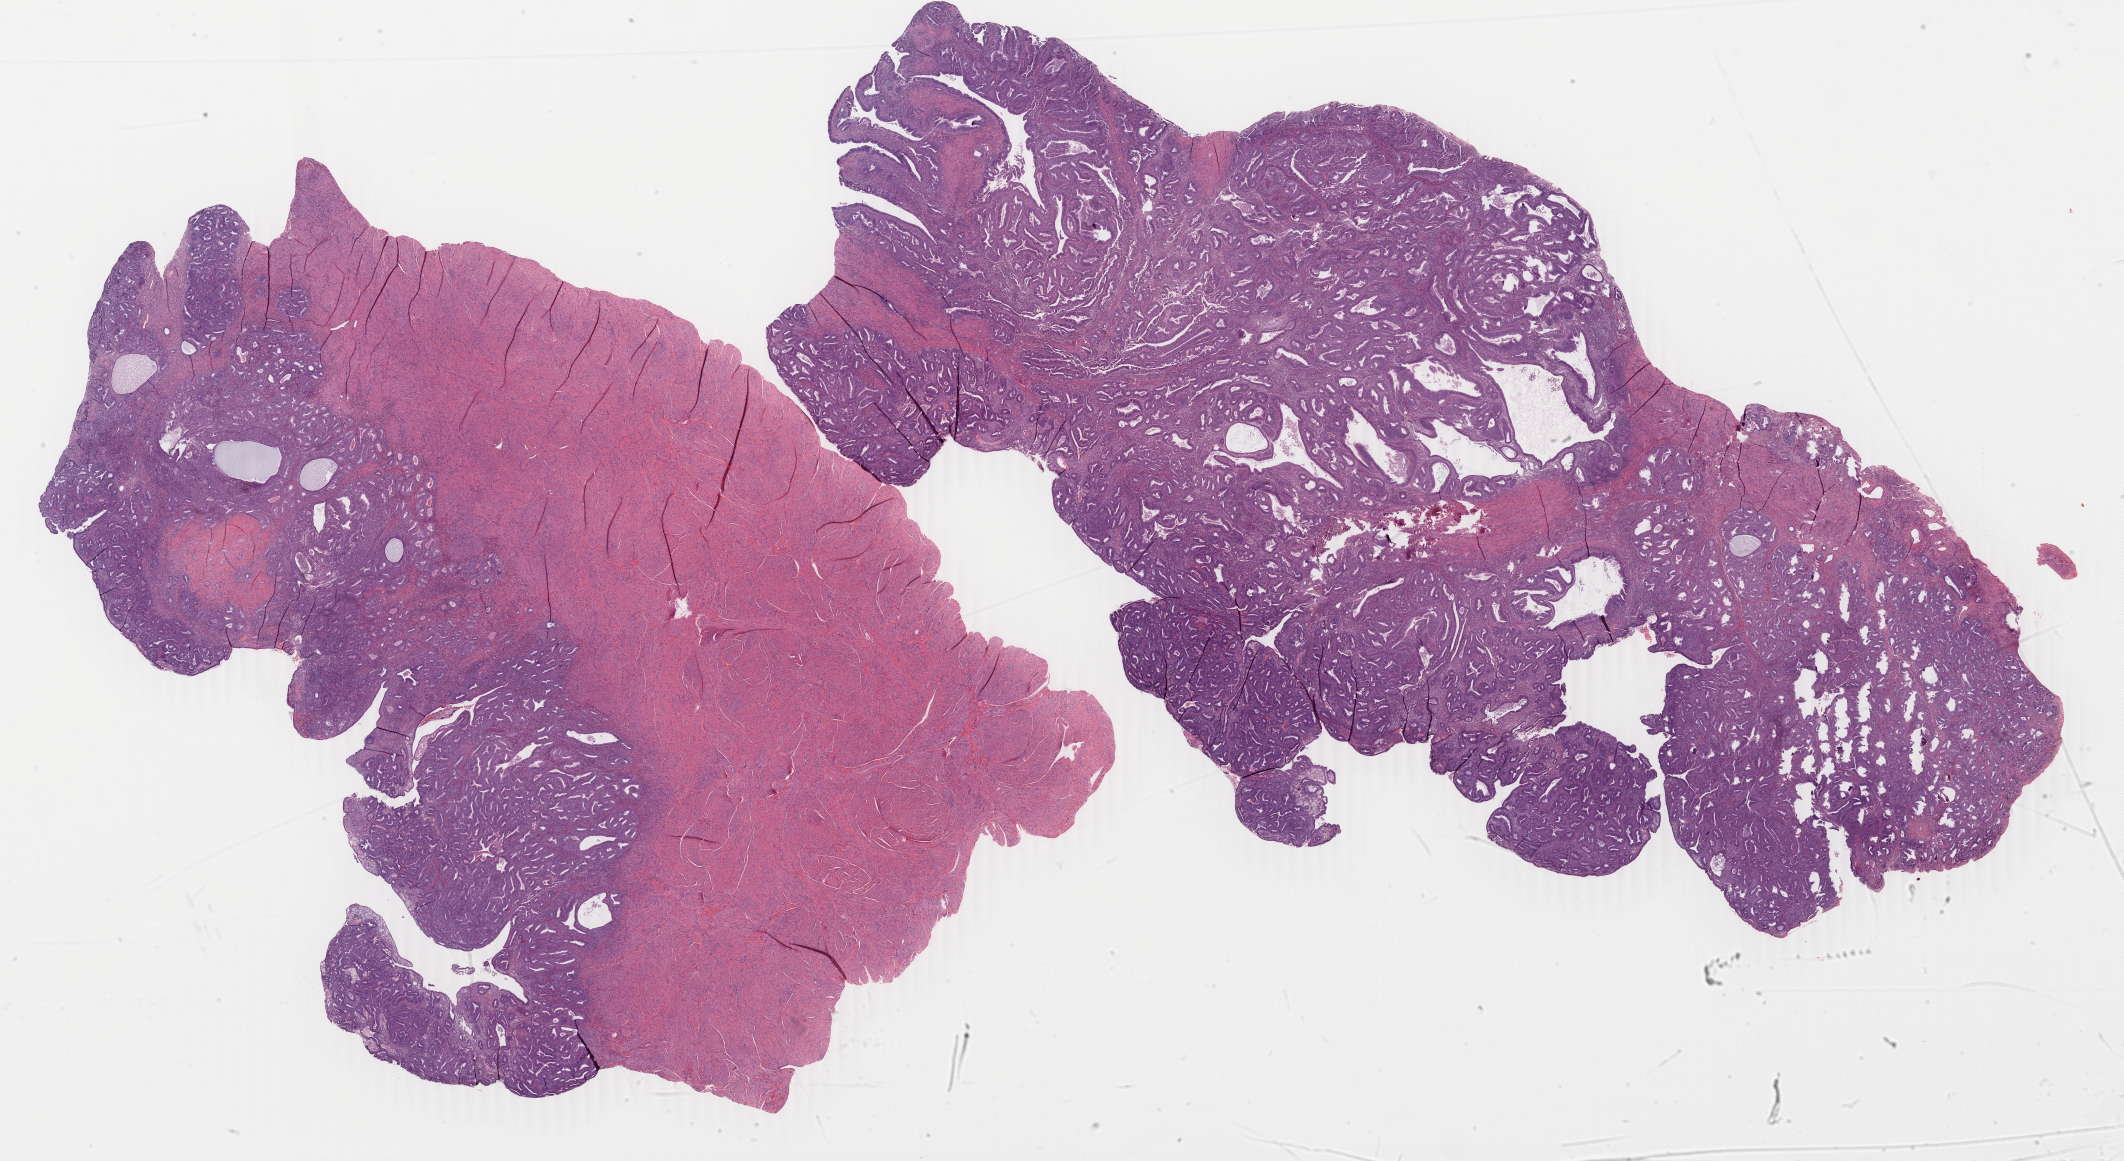
Digitized Hematoxylin and eosin (H&E) stained tissue section (whole slide) — whole scanned area (about 33.8 x 18.5 mm, acquisition: 40x scan) shown as a low-resolution overview, formalin-fixed paraffin-embedded (FFPE) diagnostic section, primary tumour sample from the uterus. Female, age 38 years at initial diagnosis.
Histologic diagnosis: Endometrioid adenocarcinoma, NOS.